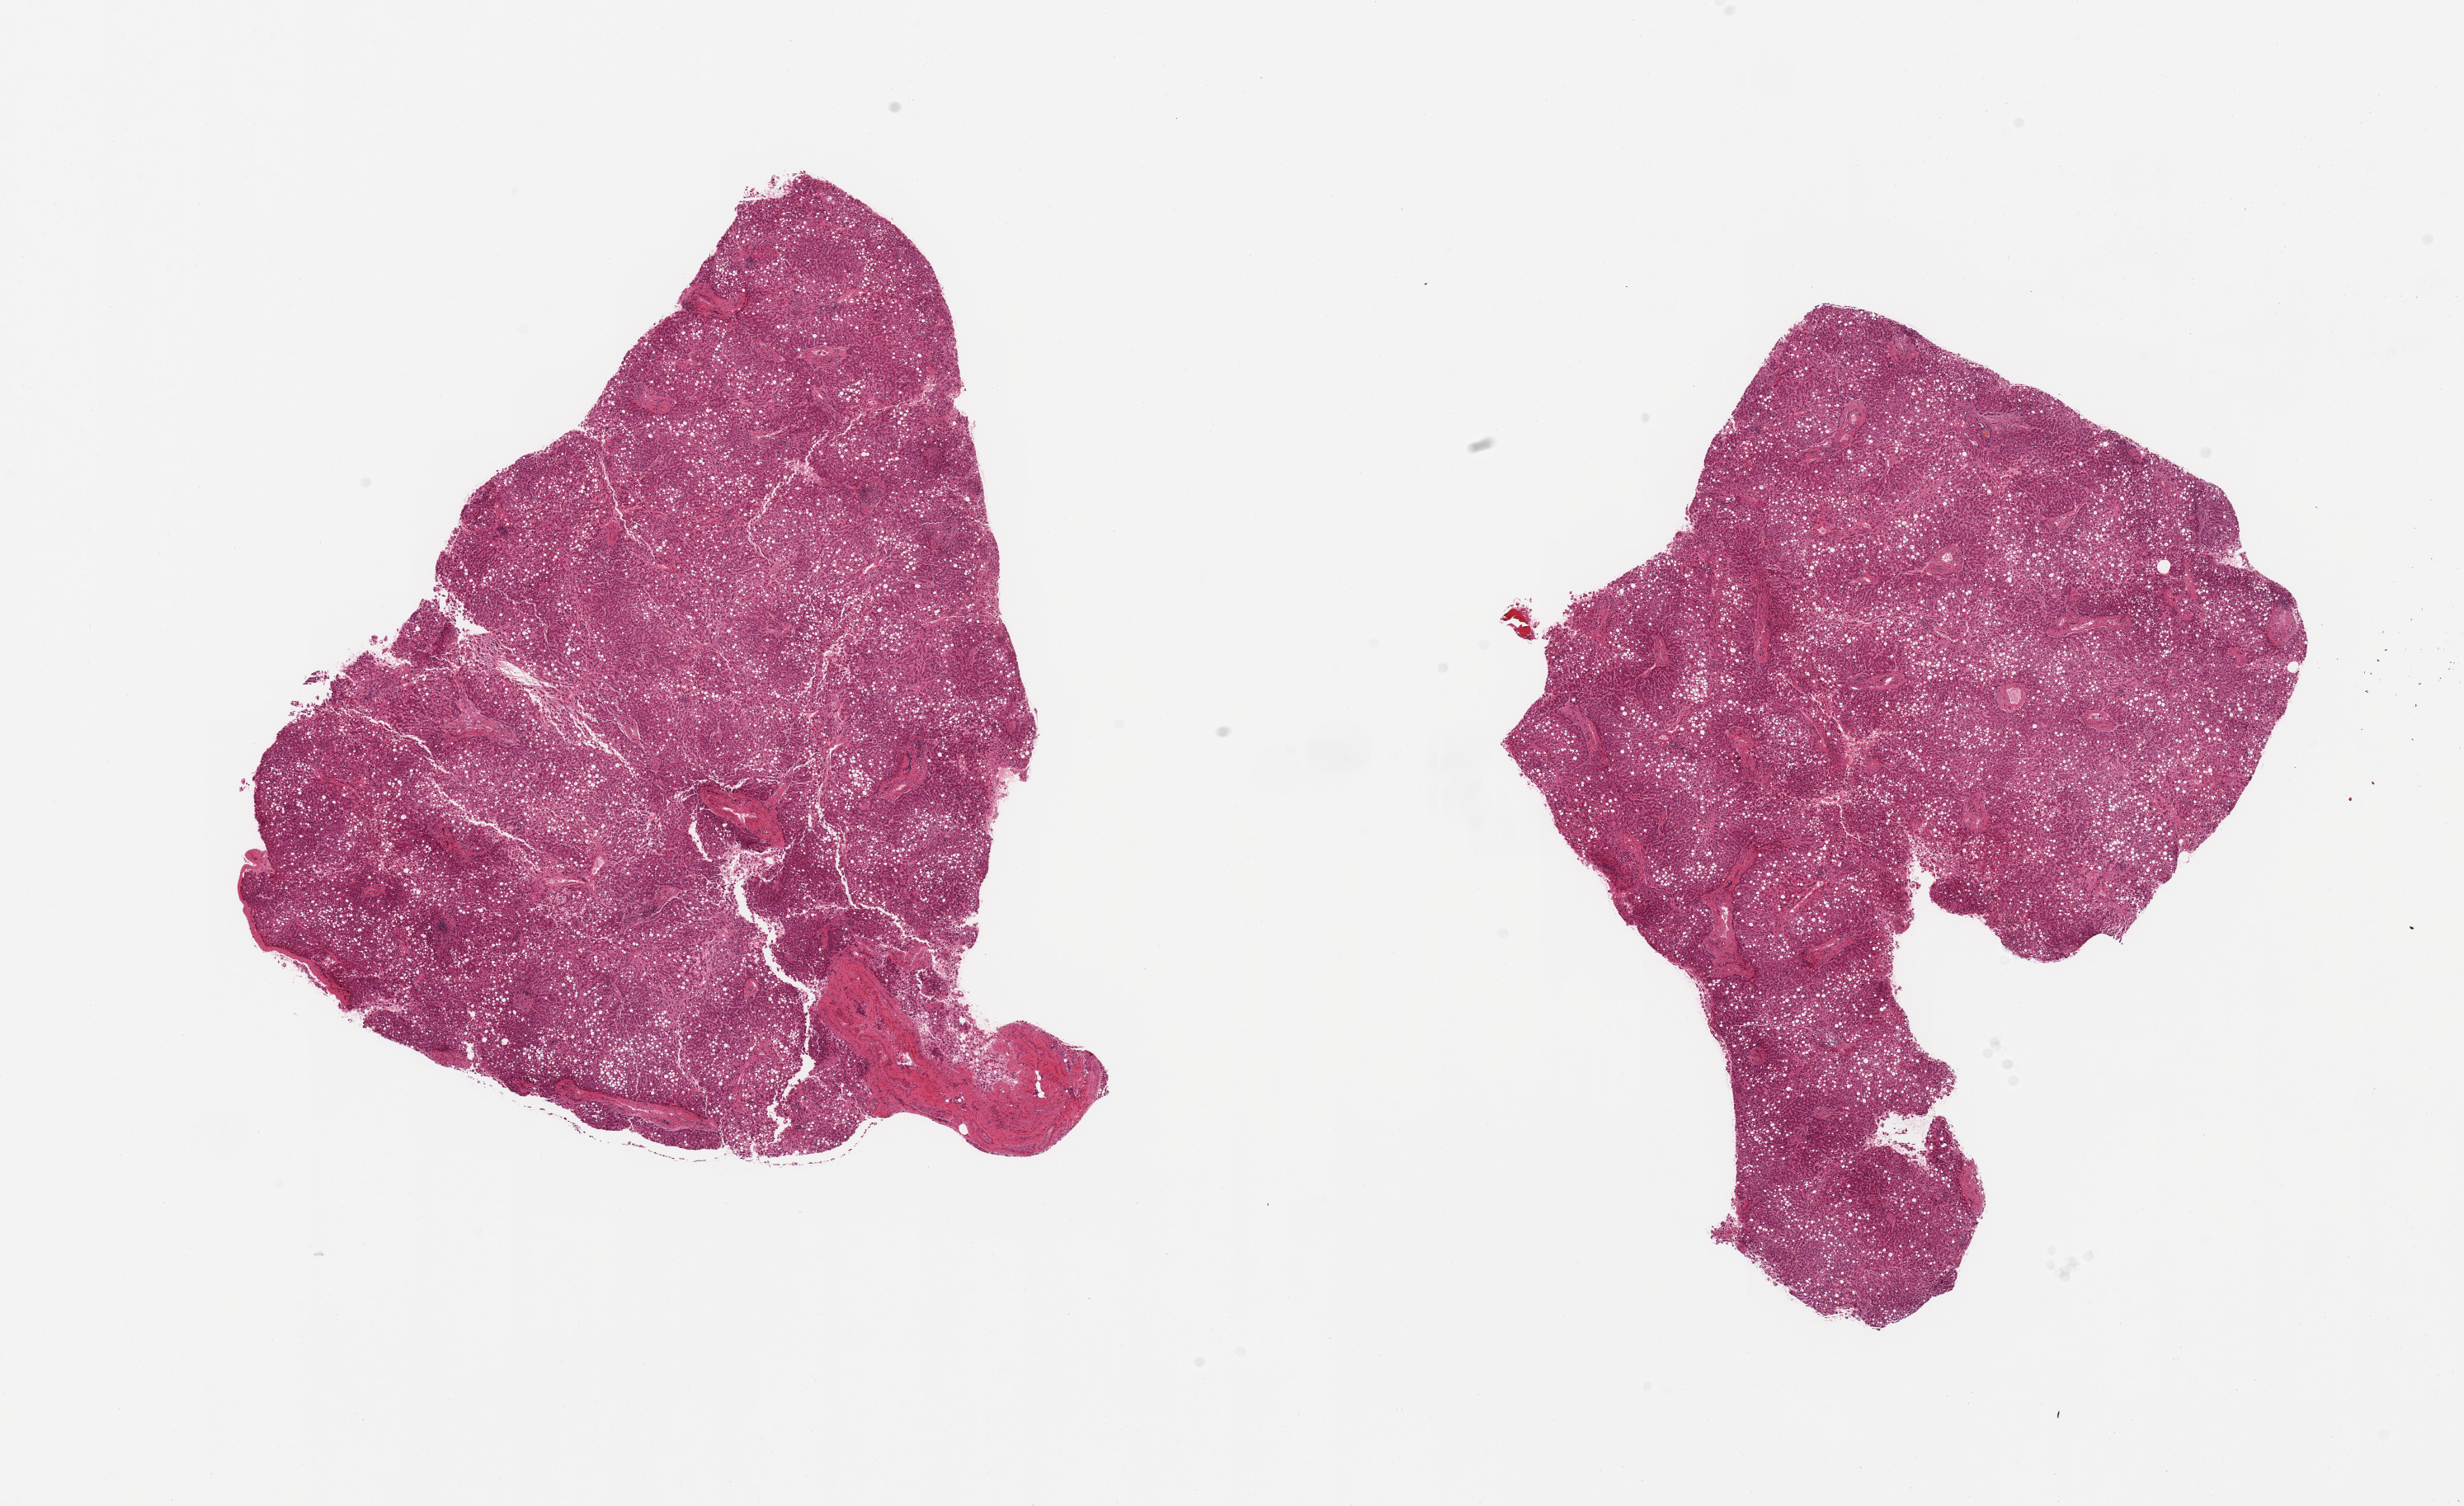
Haematoxylin and eosin whole-slide image, brightfield — low-resolution overview of the scanned area, about 23.6 x 14.4 mm, PAXgene-fixed, paraffin-embedded tissue, sampled site (target tissue): liver, donor tissue sample.
Pathologist's review note for this sample: 2 pieces; moderate macrovesicular steatosis; large blood vessel occupies 10% of 1 piece.